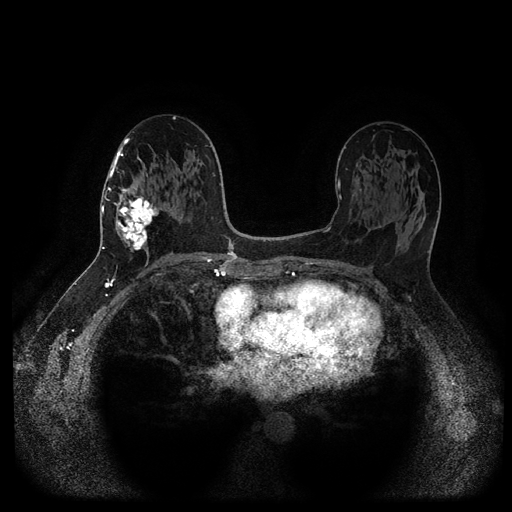
Breast MRI (dynamic contrast-enhanced, multi-phase), one axial slice; slice 54 of 116 in the series (ordered by position); dynamic contrast-enhanced series, time point 2 of 5 at this slice position (early post-contrast); 1.5 T; TE 2.6 ms, TR 5.3 ms; 512 × 512 image matrix. Female patient, age 58 years.
Structures marked on this image (semi-automatic segmentation, software-assisted and operator-edited):
- breast lesion (labelled 'tumour' in the annotation; benign lesions carry a separate 'benign' label): bounding box [x1, y1, x2, y2] px = [114, 185, 160, 254]